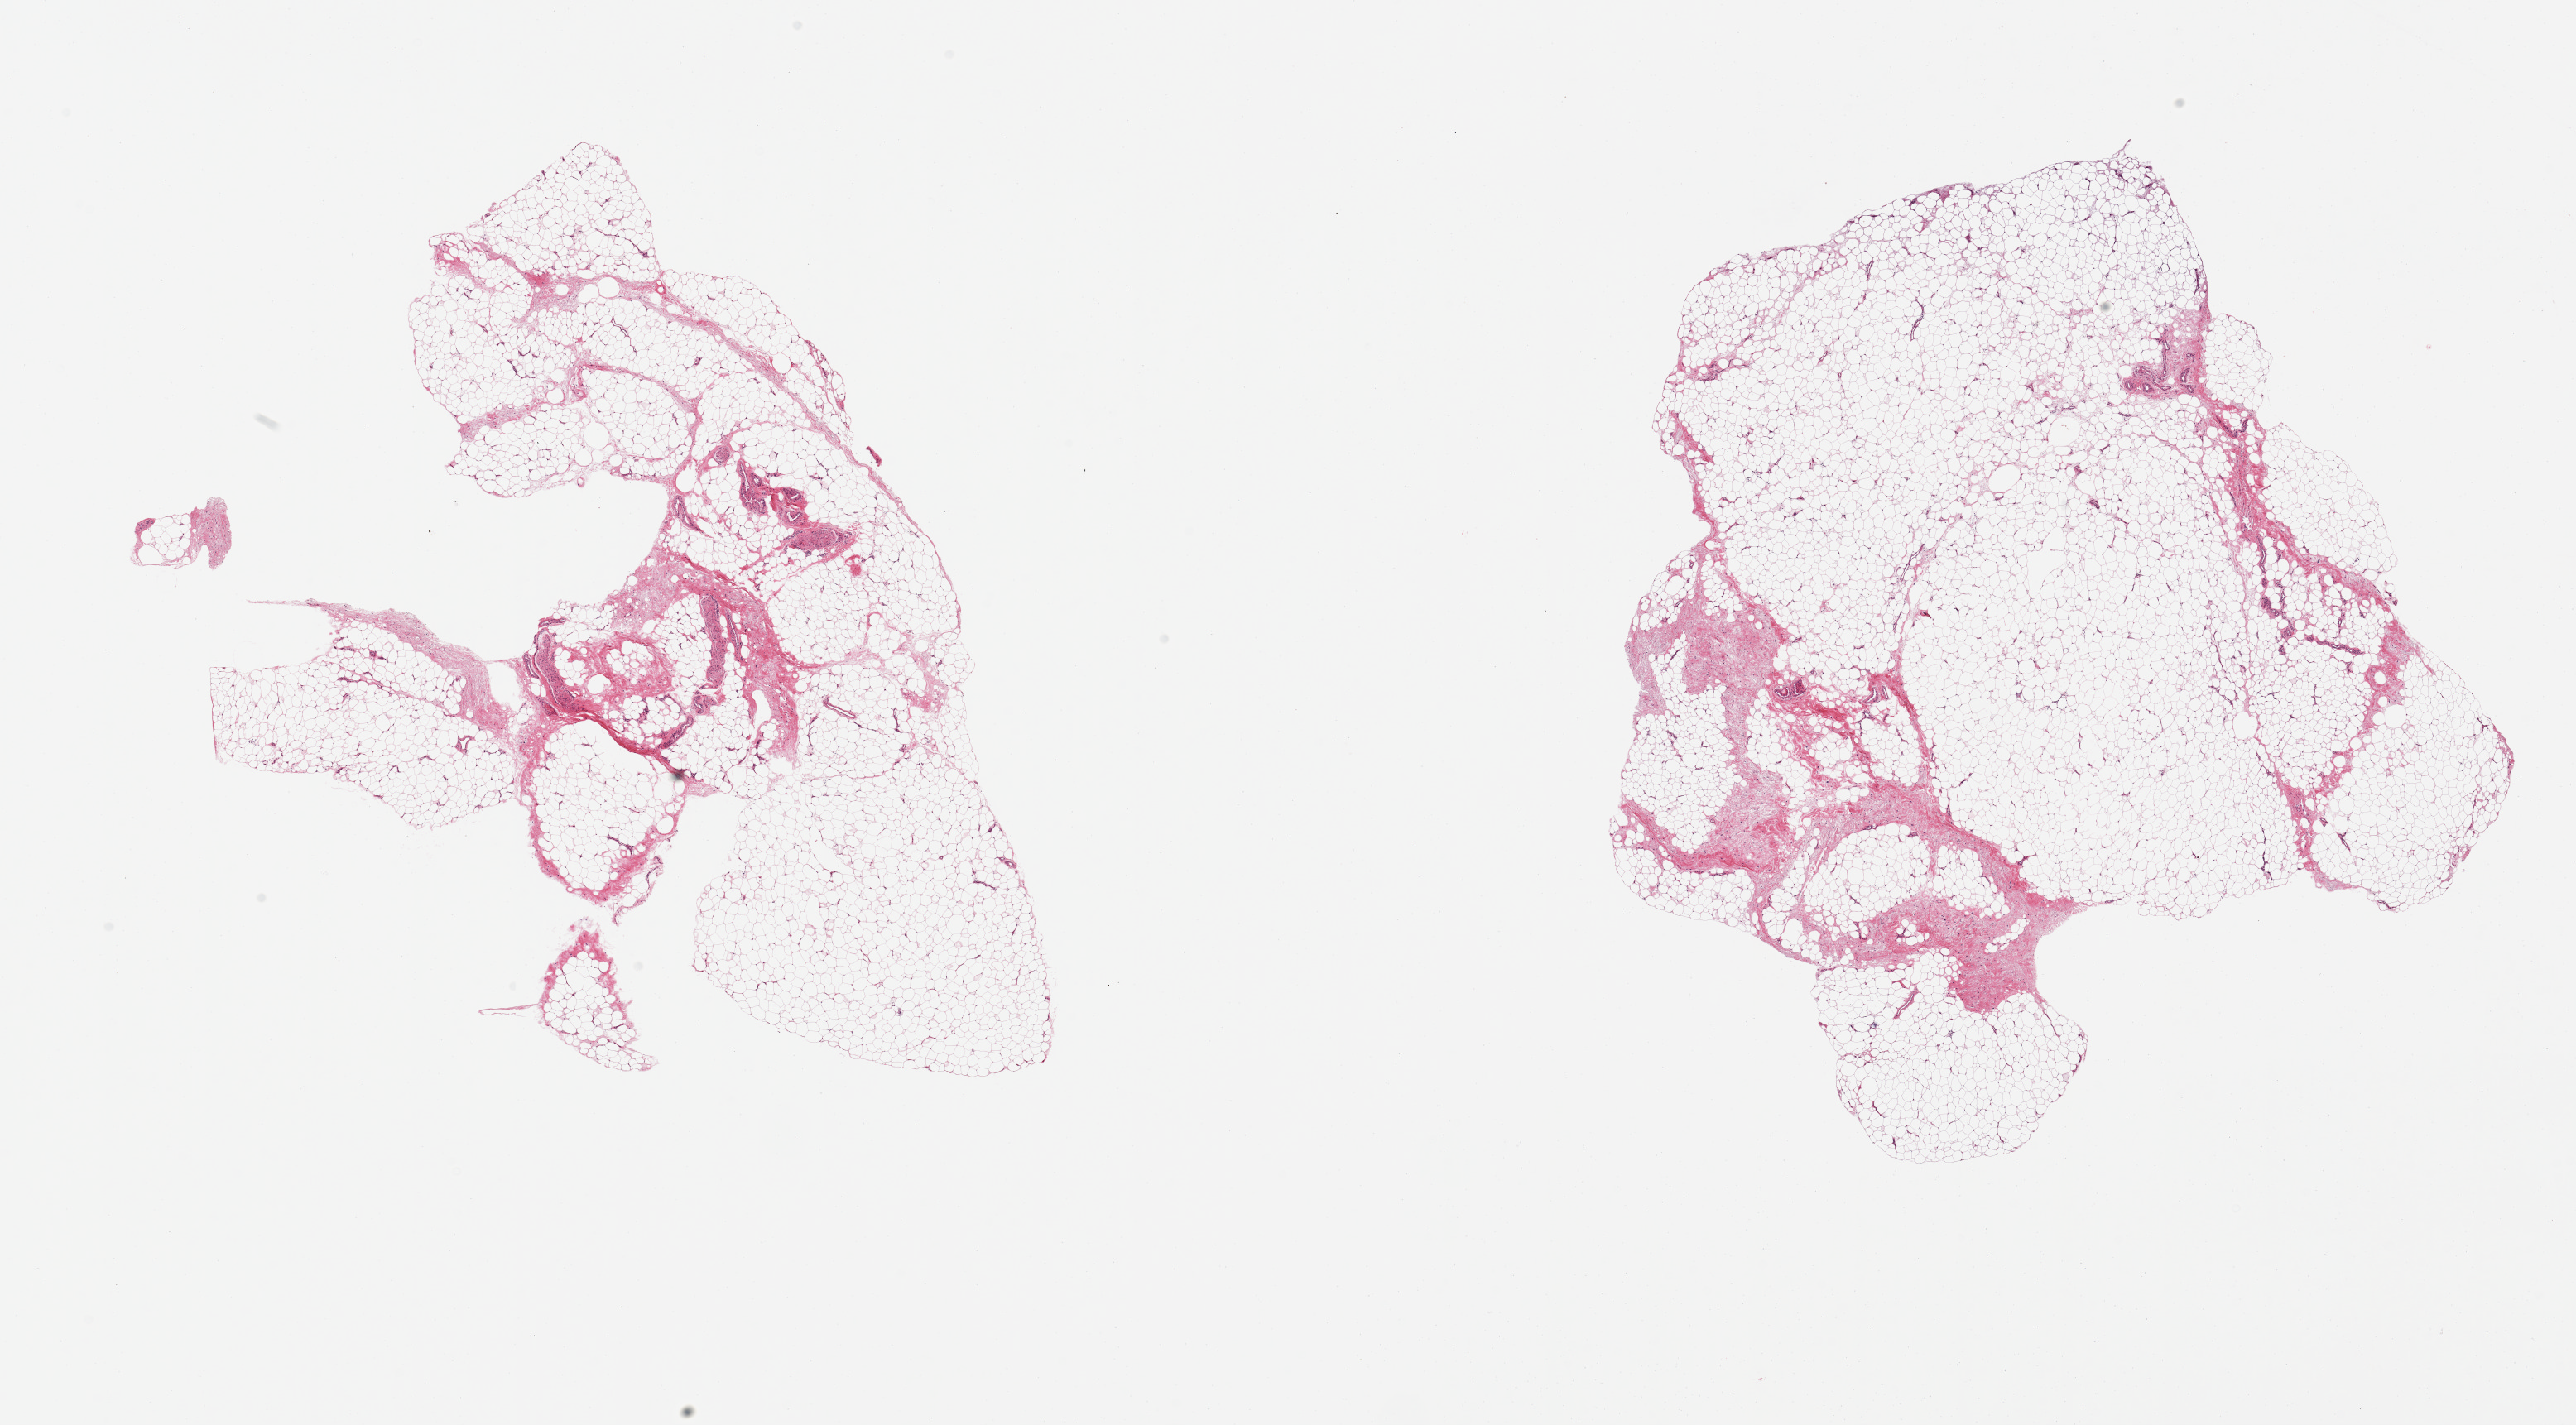
Digitized H&E-stained section, brightfield, a low-resolution overview of the entire scanned area, about 24.6 x 13.6 mm, PAXgene-fixed paraffin-embedded (PFPE) section, section of adipose tissue (target tissue), tissue donor sample.
- reviewer comment on this tissue sample: 2 pieces fascia is ~10-15%